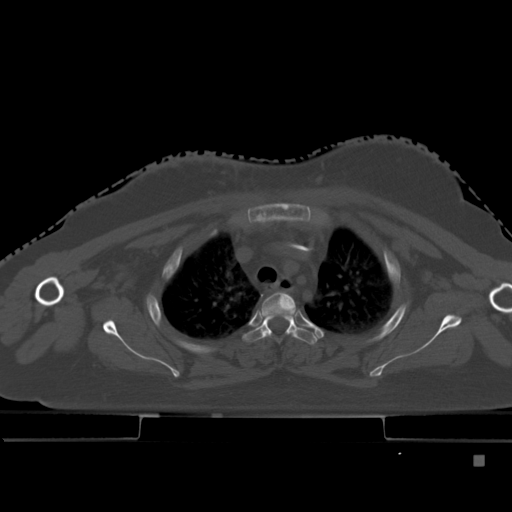
CT including the spine, one axial slice; position 350 of 495 along the scan axis; bone window (W 1800 / L 400 HU); 1.5 mm slice thickness; 512 × 512 image matrix, field of view 404 × 404 mm. Female patient, age 33 years. From the clinical record (not read from this slice): primary cancer: breast; vertebrae with lytic lesions (as recorded): T1.
Annotated regions visible in this slice (semi-automatic segmentation, software-assisted and operator-edited):
- T2 vertebra: bounding box (x1, y1, x2, y2) in pixels: (261, 291, 295, 332)
- T3 vertebra: (244, 316, 319, 344)